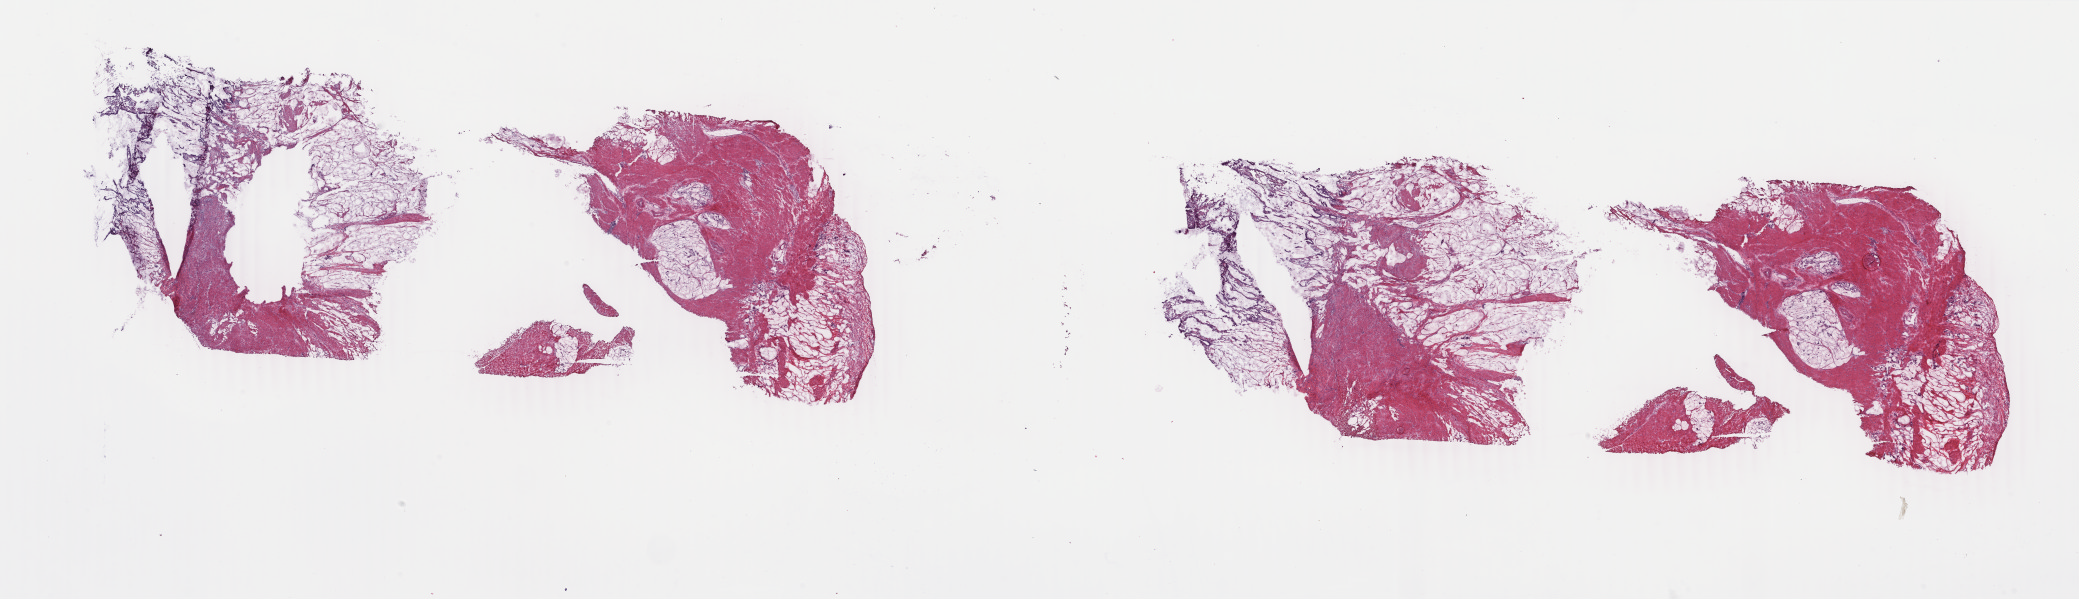
Whole-slide histology image, H&E-stained, whole scanned area (about 33.1 x 9.5 mm) shown as a low-resolution overview; frozen section from the top of the tissue portion; primary tumour sample from the stomach. Male, age 56 years at initial diagnosis. Histologic grade: G3 (poorly differentiated). Pathologist review of this section (percent, as recorded): tumour cells 40%, tumour nuclei 70%, normal cells 0%, stromal cells 50%, necrosis 10%. Infiltration values recorded for this section: lymphocyte infiltration 2%, monocyte infiltration 0%, neutrophil infiltration 1%.
Diagnosis: Mucinous adenocarcinoma (gastric antrum). Lymph nodes positive (case pathology): 1 of 5 examined. AJCC pathologic stage: IIIA. TNM: T4a N1 M0.